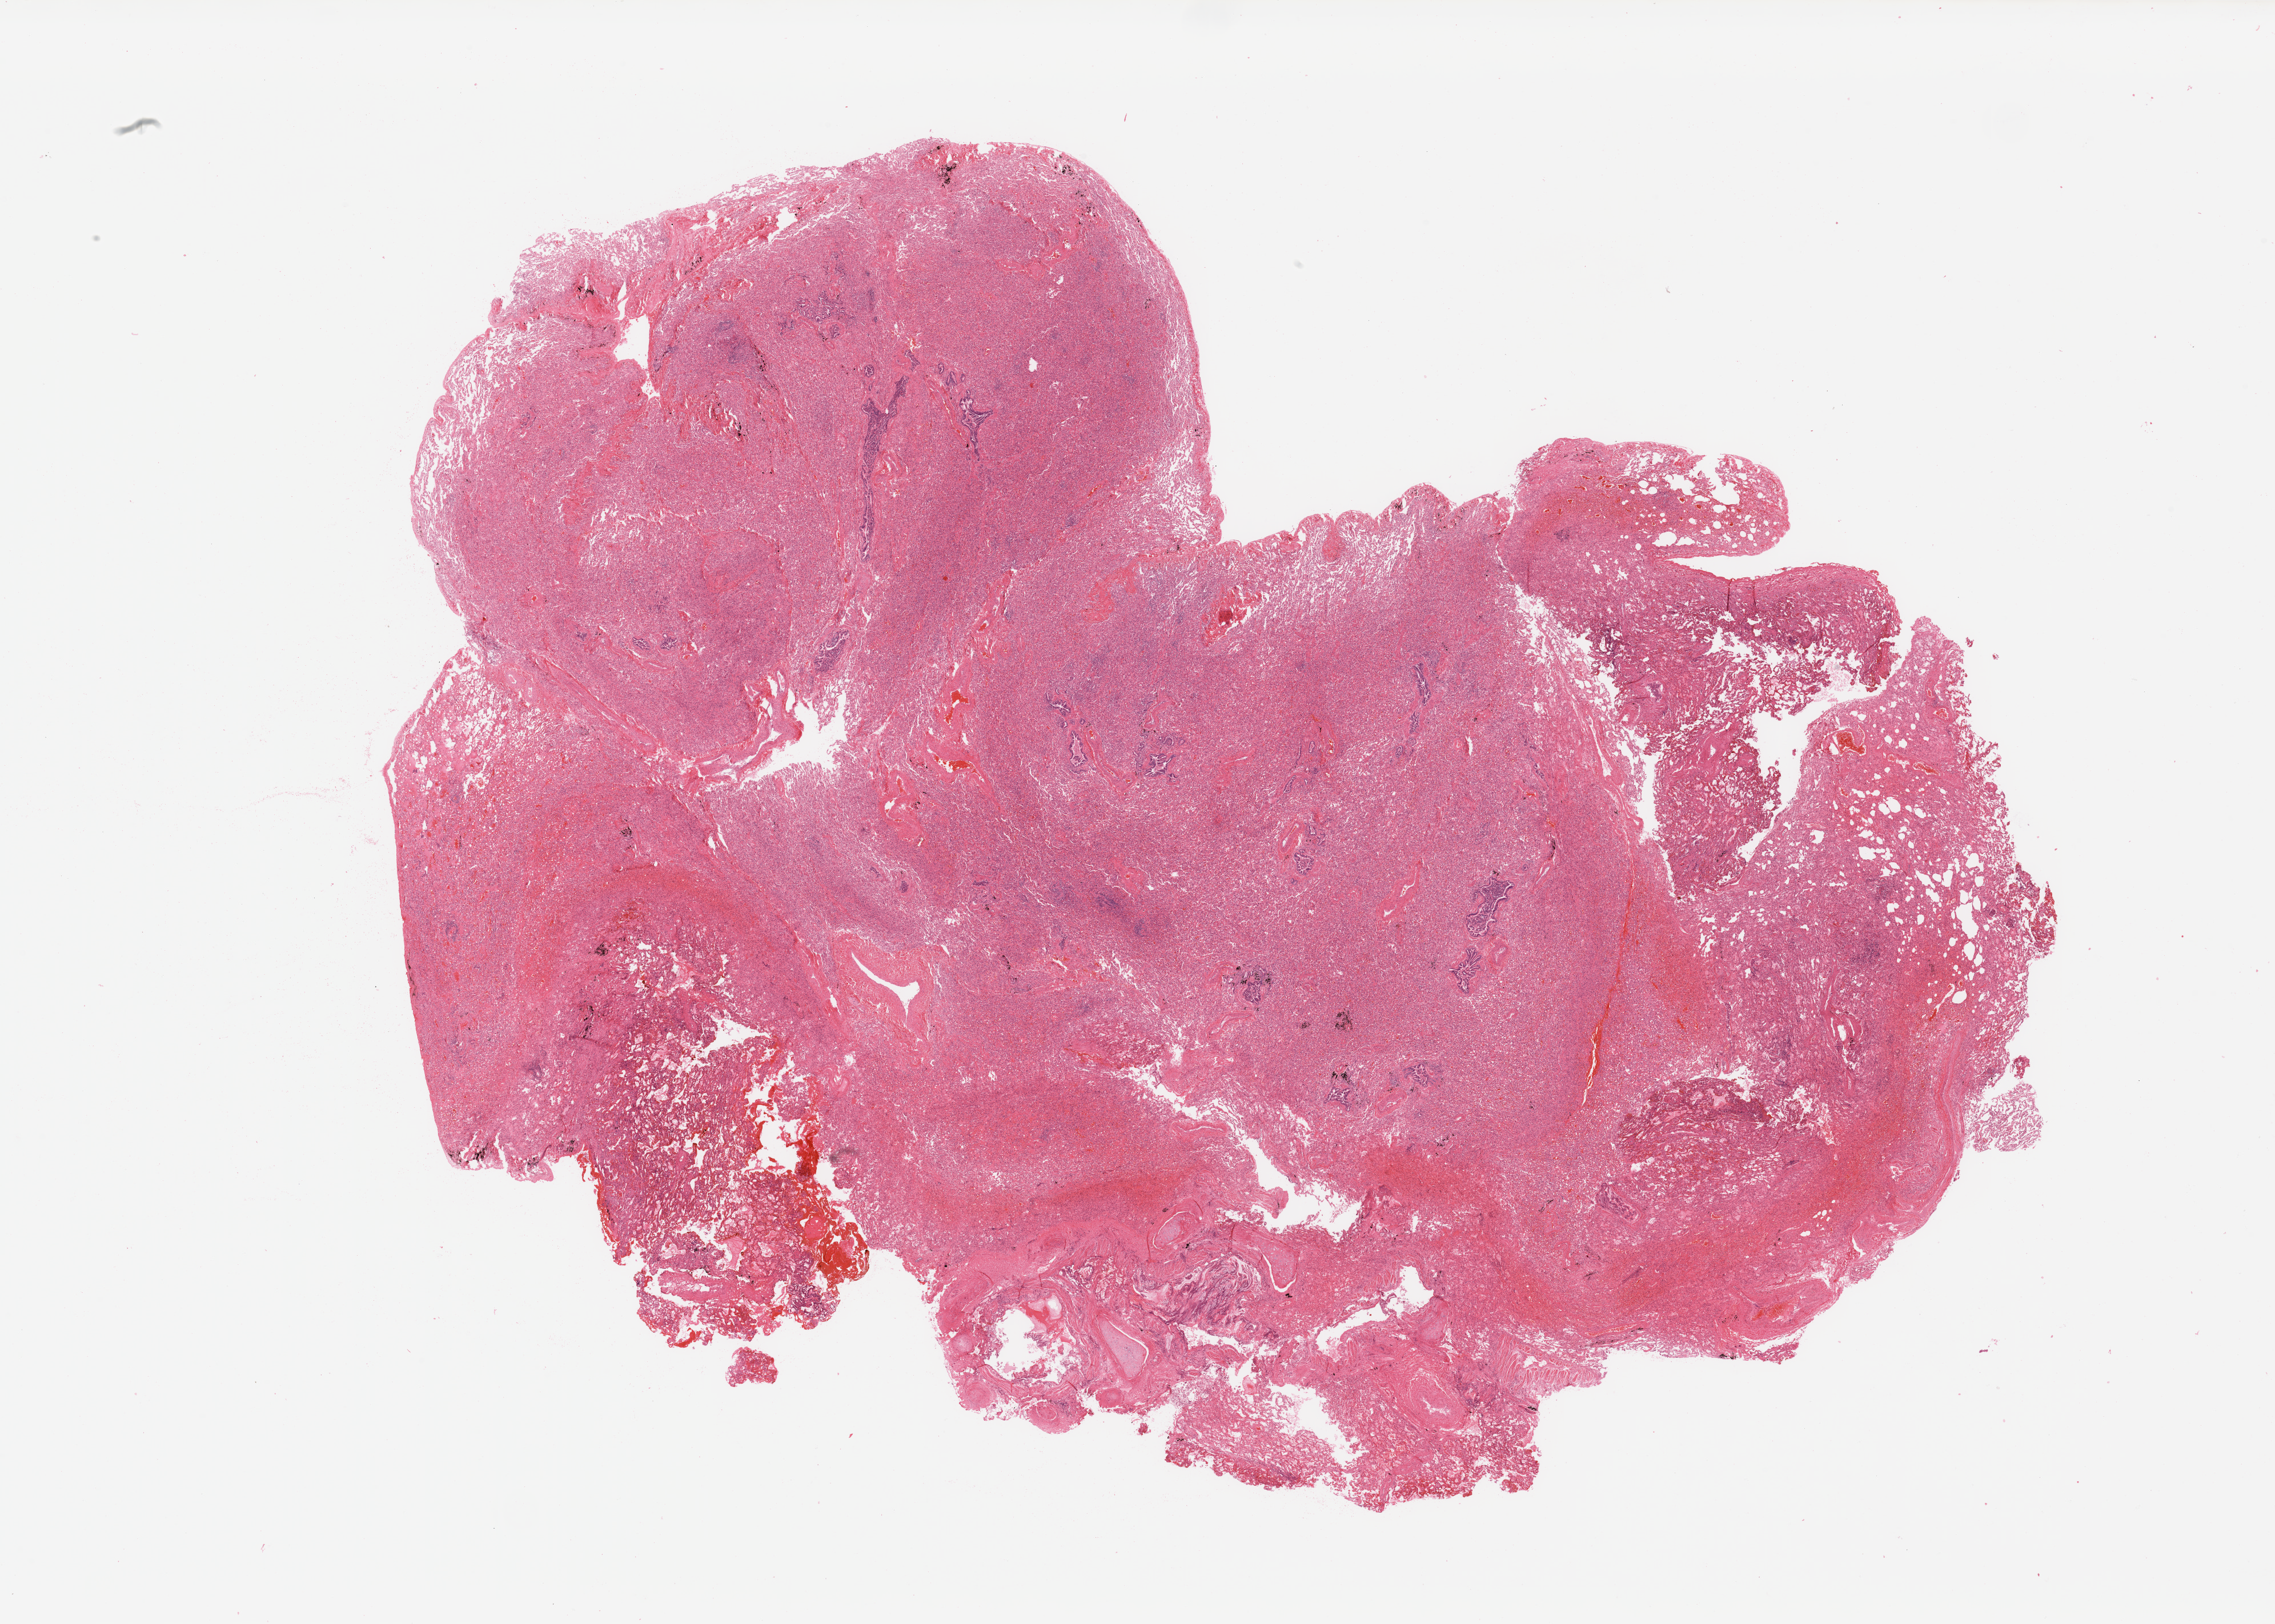
Digitized H&E-stained tissue section (whole slide) — shown as a low-resolution overview of the whole scanned area (about 31.5 x 22.5 mm, acquisition: 20x scan); normal (non-tumour) tissue sample, lung. Patient: female, age 47 years.
This section: normal (non-tumour) tissue from the same patient. Patient diagnosis: Adenocarcinoma, NOS.